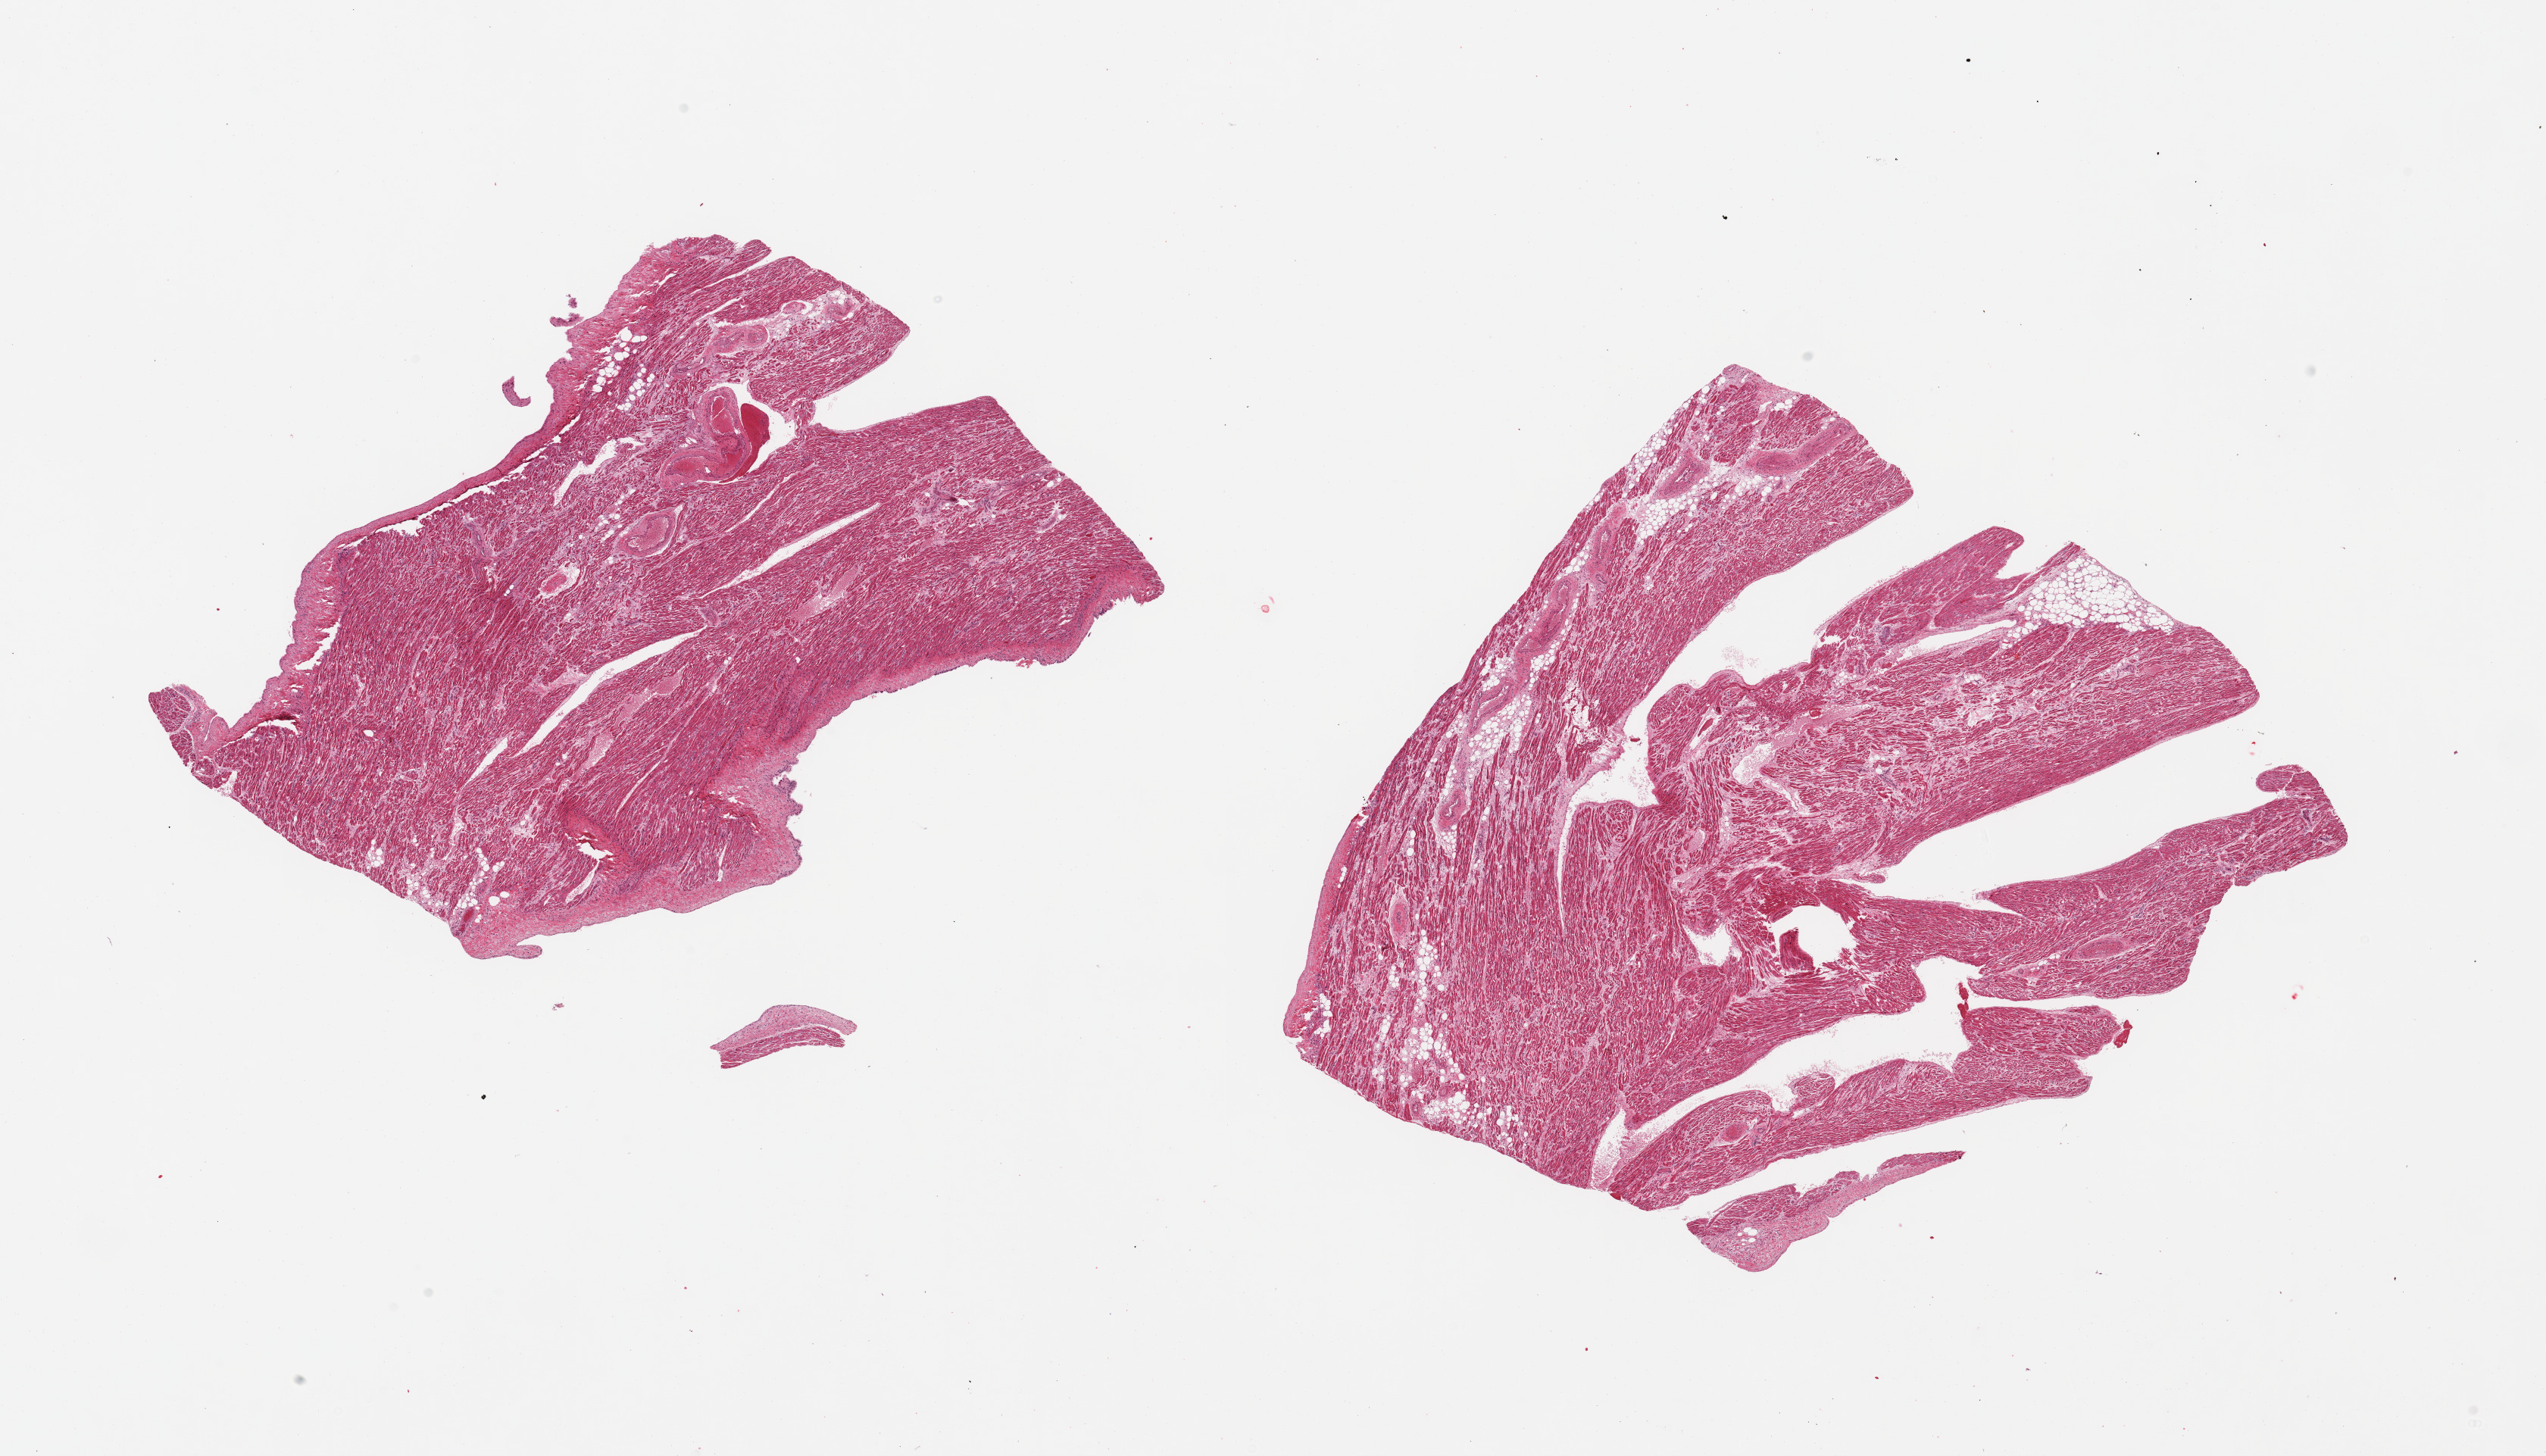
Haematoxylin and eosin whole-slide image, shown as a low-resolution overview of the whole scanned area (about 26.6 x 15.2 mm, from a 20x scan), PAXgene-fixed, paraffin-embedded tissue, target tissue: auricular appendage, donor tissue sample. Donor sex: female.
Pathologist's review note for this sample: 2 pieces; 5% fatty content.